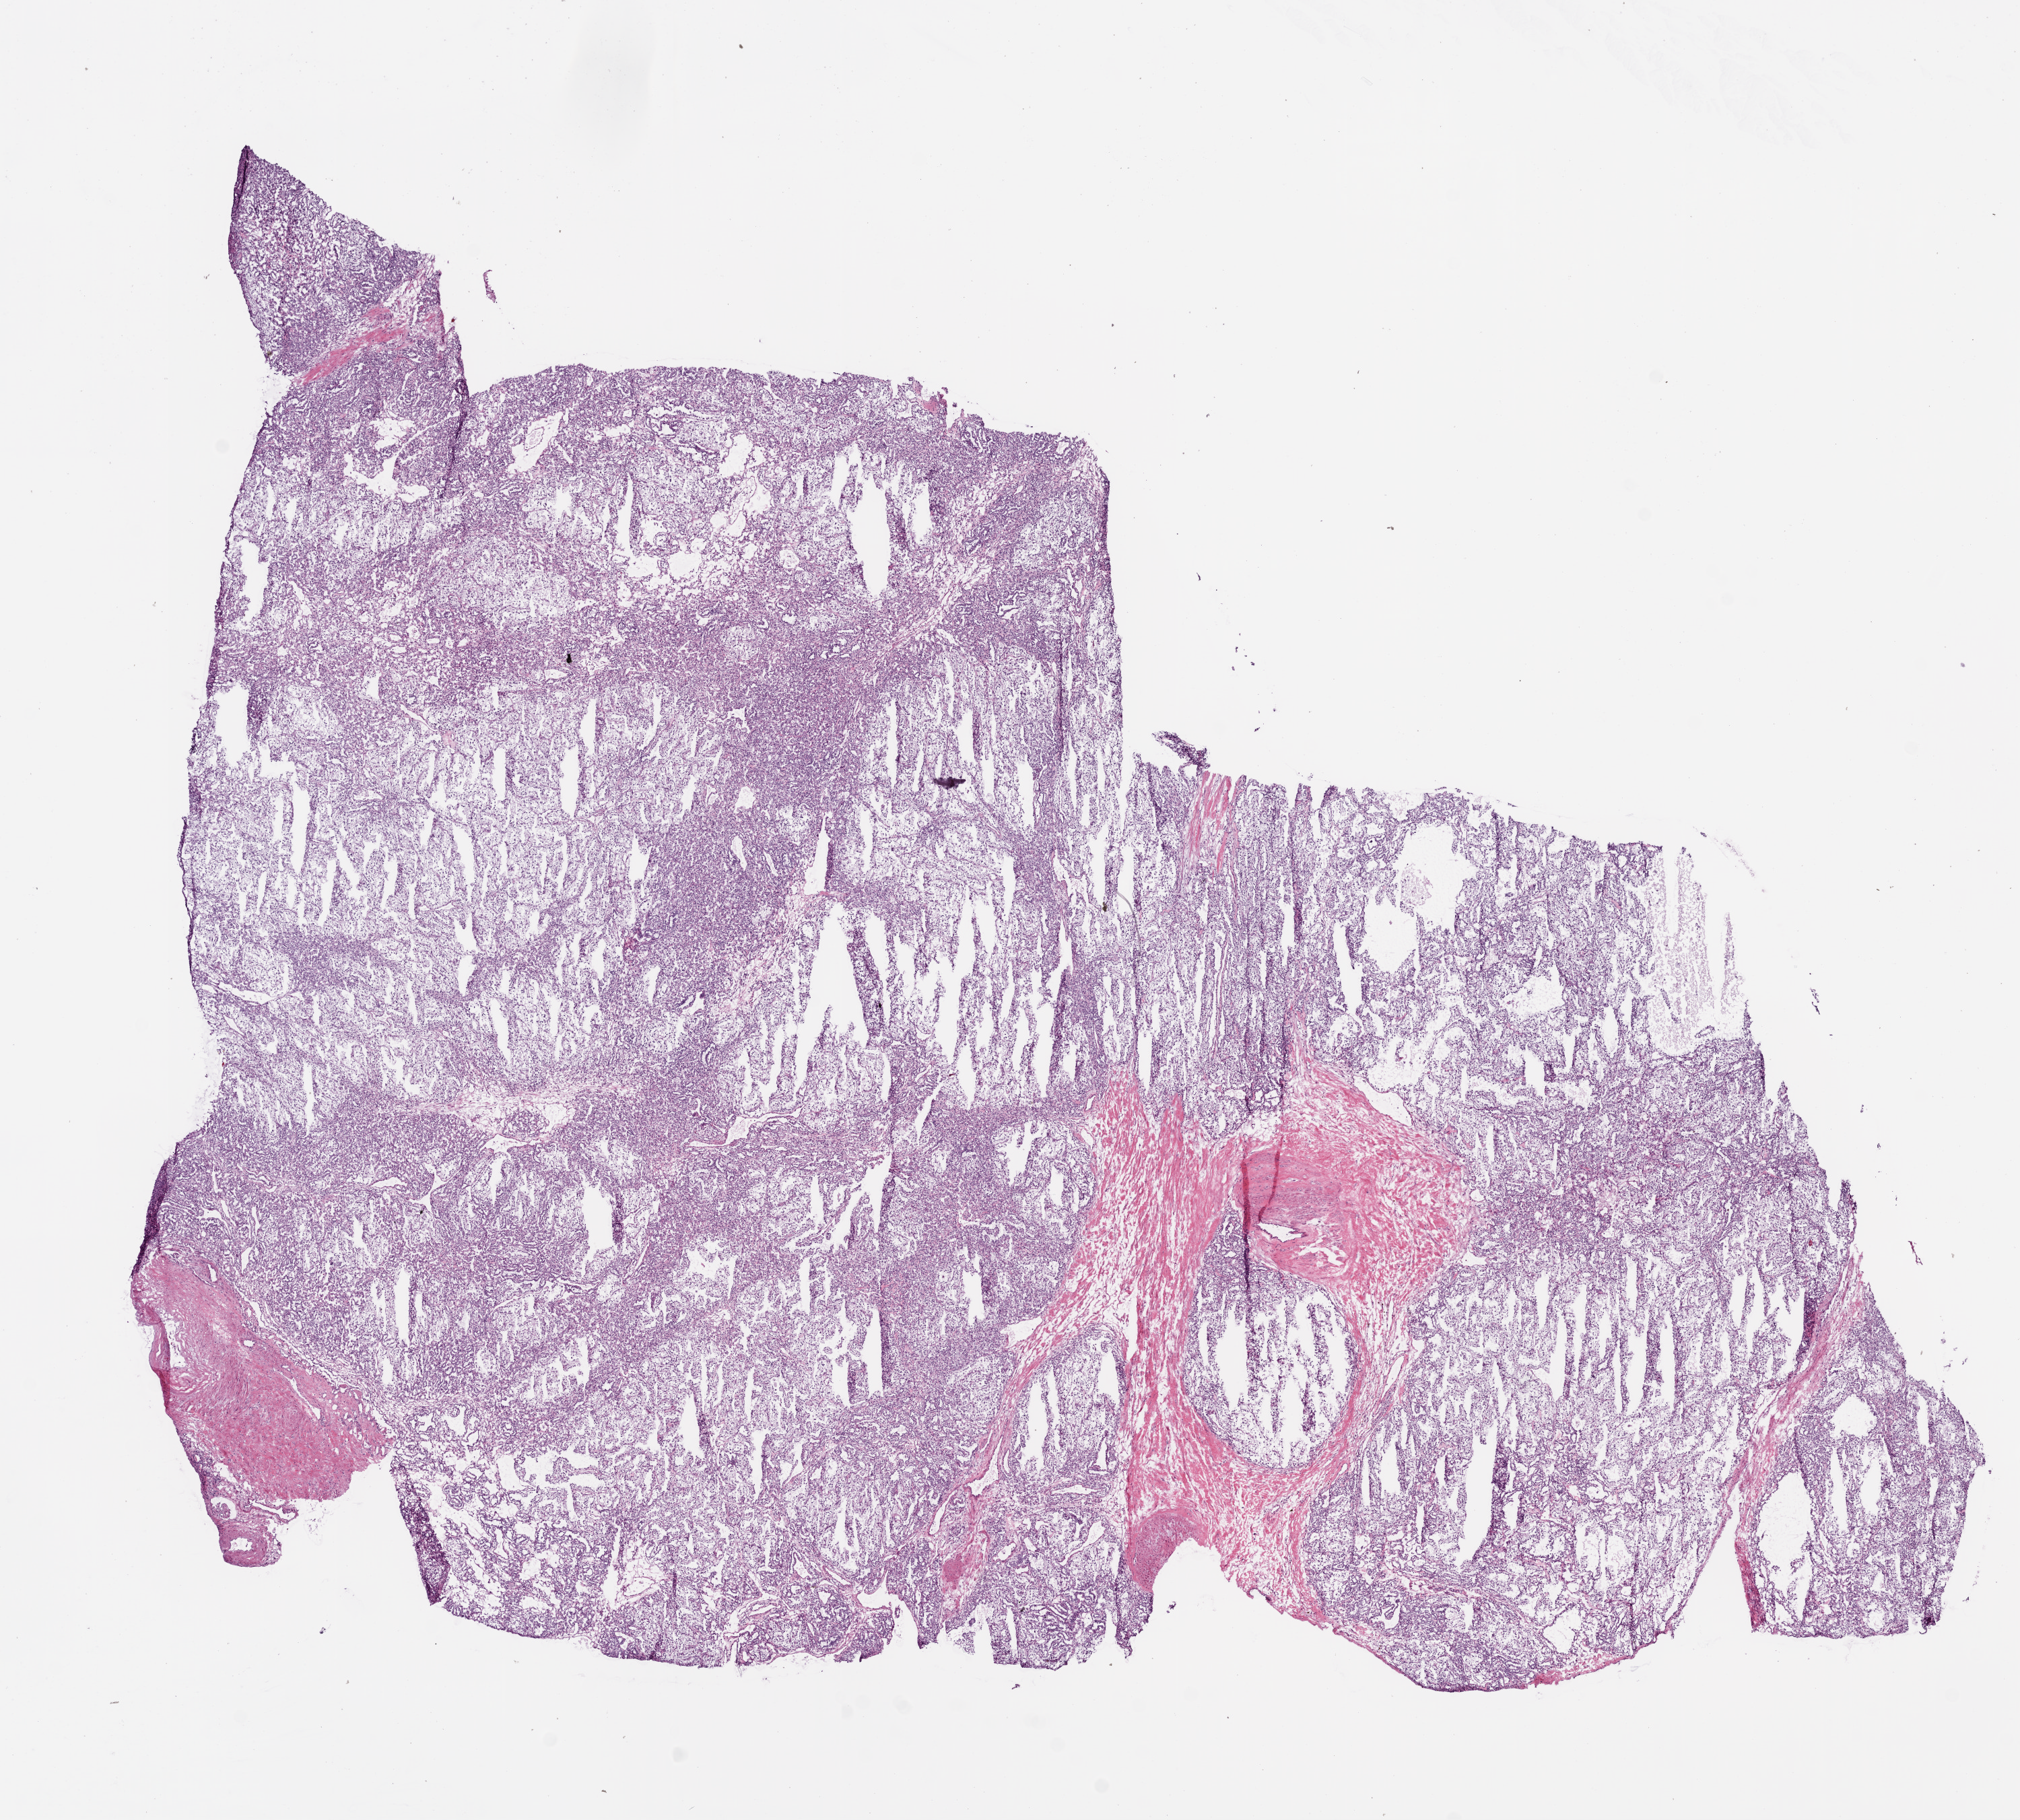
Whole-slide histology image, Hematoxylin and eosin (H&E) stained, whole scanned area (about 12.0 x 10.8 mm, slide scanned at 20x) shown as a low-resolution overview; frozen section; kidney, primary tumour sample. Patient: male, age at initial diagnosis 62 years. Histologic grade: G2 (moderately differentiated). Slide review estimates, as recorded: tumour cells 95%, tumour nuclei 90%, normal cells 0%, stromal cells 5%, necrosis 0%. Inflammatory infiltration, as recorded: lymphocyte infiltration 2%, monocyte infiltration 0%, neutrophil infiltration 1%.
TNM: T1 N0 M0. Laterality: right. AJCC pathologic stage: I (7th edition). Diagnosis: Clear cell adenocarcinoma, NOS.